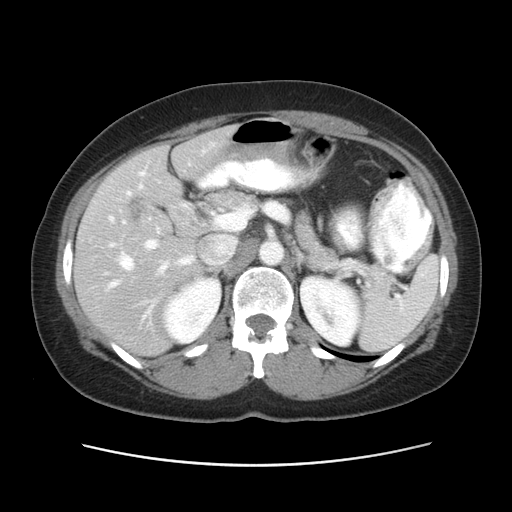
Contrast-enhanced abdominal CT, one axial slice; slice 31 of 52 in the series (ordered by position); reconstruction kernel STANDARD; 120 kVp; intravenous contrast given; soft-tissue window (W 400 / L 40 HU); 5 mm slice thickness; 512 × 512 image matrix, field of view 362 × 362 mm. Female patient, age 48 years. Case-level facts recorded for this patient, not image findings: diagnosis: colorectal cancer liver metastases, imaged before liver resection; multiple liver metastases: yes; largest metastasis: 4.5 cm; disease in both lobes: yes.
Structures marked on this image (expert manual segmentation):
- hepatic veins: bounding box [x1, y1, x2, y2] px = [108, 144, 214, 289]
- liver: [76, 127, 234, 354]
- planned liver remnant (the part of the liver to remain after resection): [168, 127, 234, 185]
- portal vein (with intrahepatic branches): [127, 172, 158, 249]
- liver metastasis: [127, 197, 146, 225]